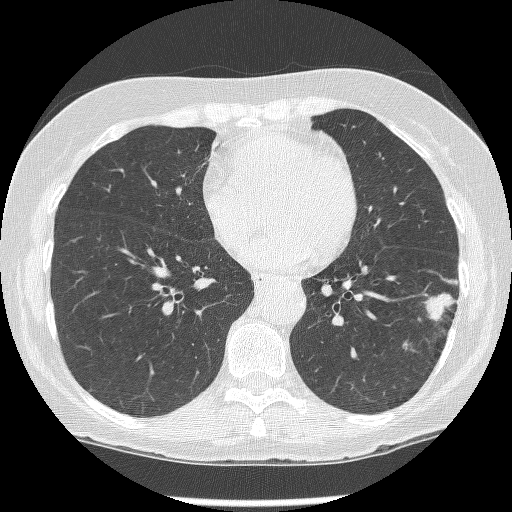
Low-dose screening chest CT, axial slice; baseline annual screen; lung window (W 1500 / L -600 HU); 1.25 mm slice thickness; lung (sharp) reconstruction kernel (BONE). Female, age 62 years at enrolment. Former smoker at enrolment.
Expert-annotated lung lesion, bounding box <414,283,460,343> (left, top, right, bottom; pixels). The screening reader recorded 2 non-calcified nodules or masses ≥4 mm on this exam (left lower lobe, left lower lobe); which of them this box marks is not recorded.